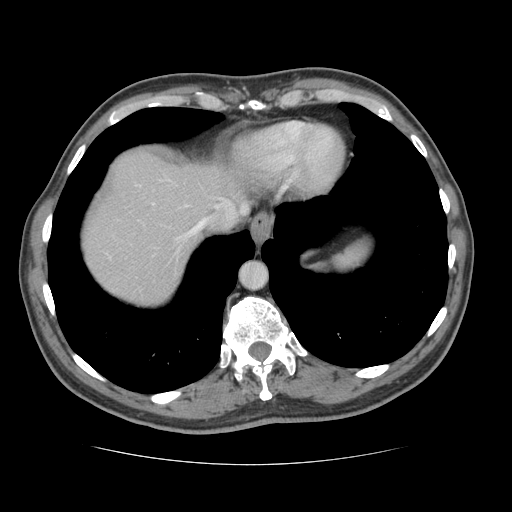
Contrast-enhanced abdominal CT, one axial slice; slice 114 of 134 in the series (ordered by position); reconstruction kernel STANDARD; 120 kVp; intravenous contrast given; soft-tissue window (W 400 / L 40 HU); 512 × 512 image matrix, field of view 377 × 377 mm. Male patient, age 68 years. From the clinical record (not read from this slice): diagnosis: colorectal cancer liver metastases, imaged before liver resection; multiple liver metastases: yes; largest metastasis: 2.2 cm.
Outlined on this slice (manually delineated by an expert):
- hepatic veins: box from (x=153, y=178) to (x=246, y=238) px
- liver: (x=82, y=151)–(x=243, y=303)
- planned liver remnant (the part of the liver to remain after resection): (x=82, y=151)–(x=244, y=300)